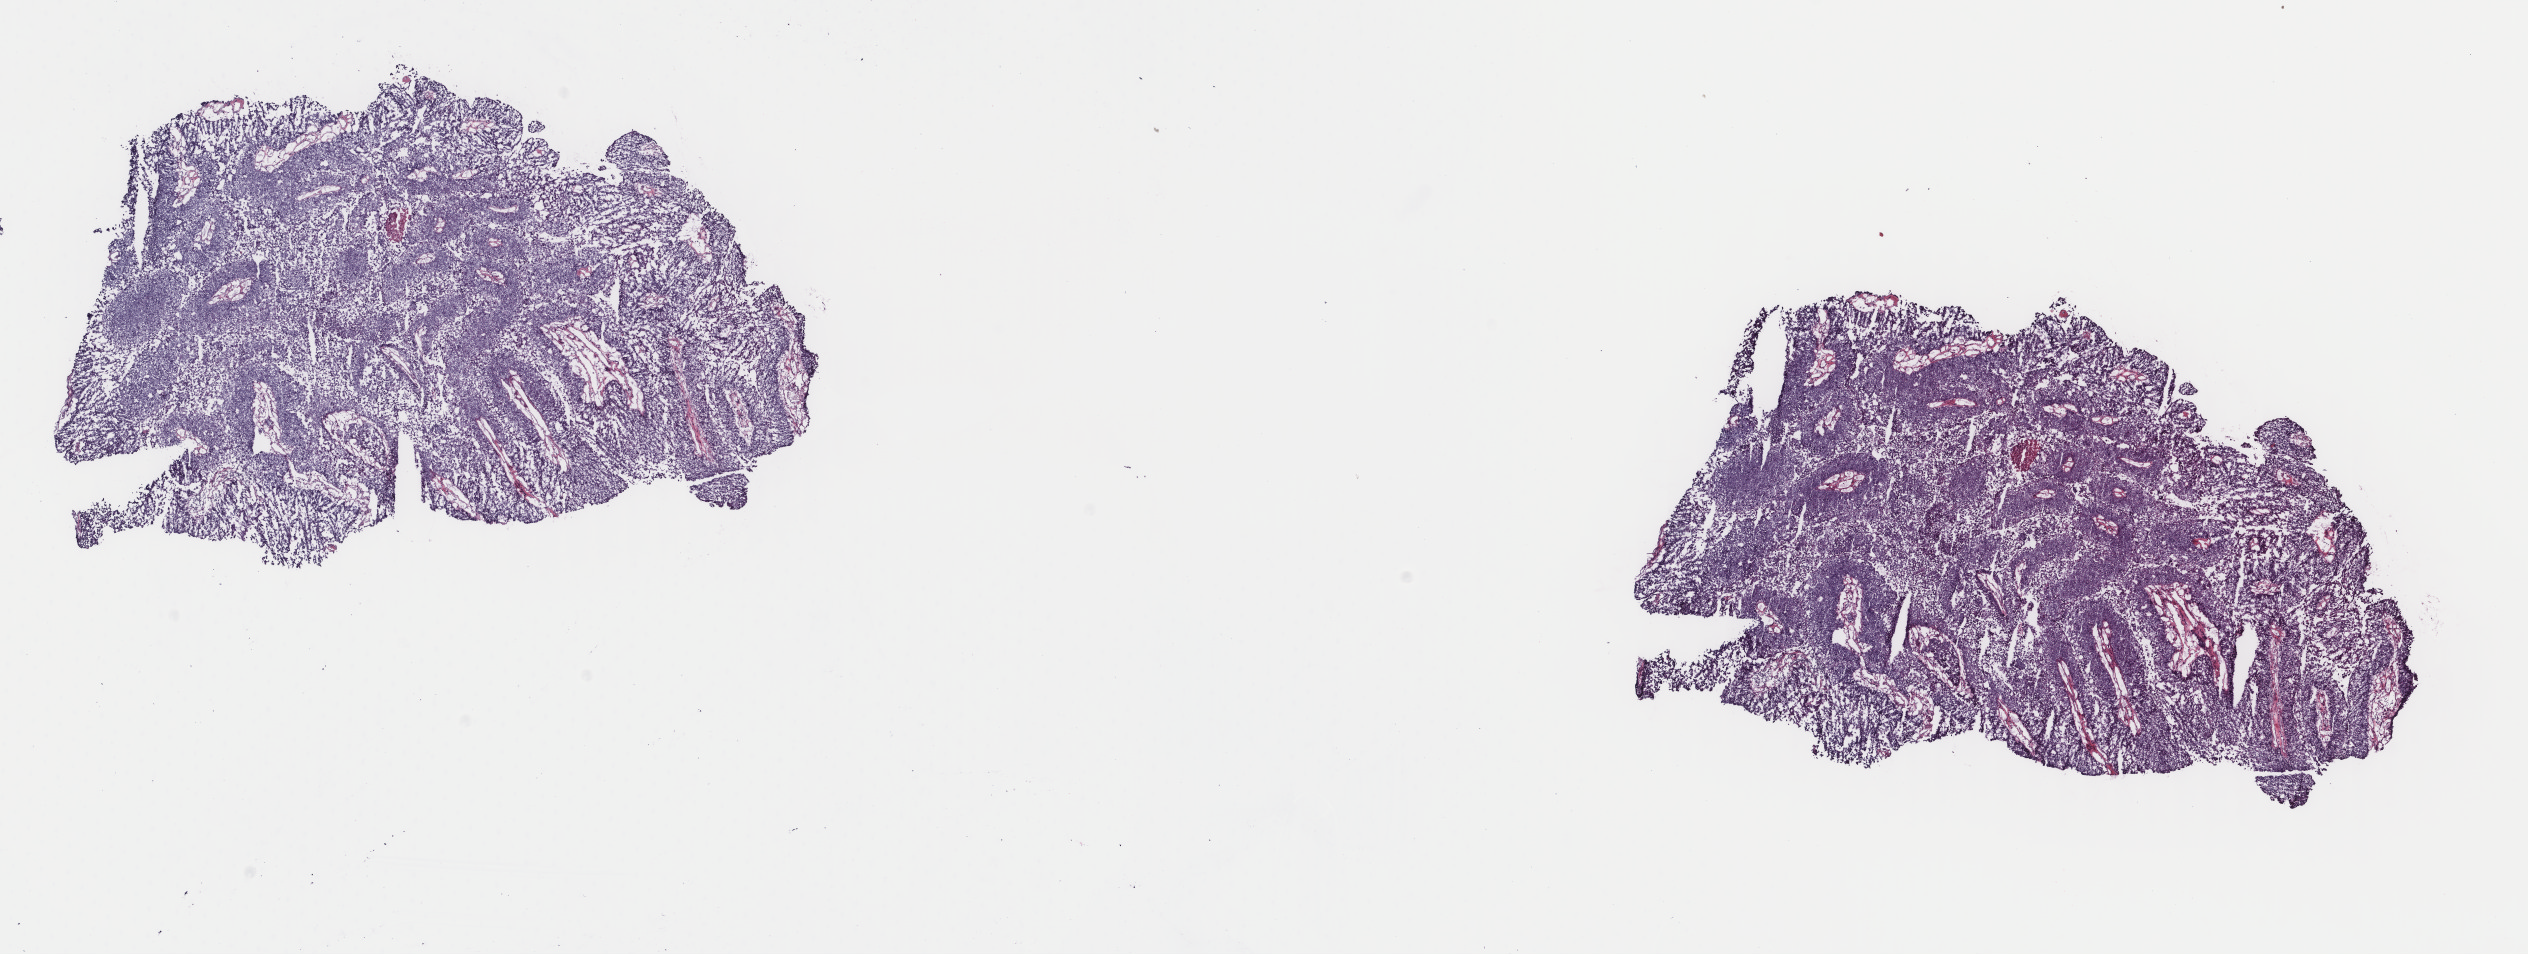
Digitized H&E tissue section (whole slide), a low-resolution overview of the entire scanned area, about 20.1 x 7.6 mm (slide scanned at 40x). Frozen section from the top of the tissue portion. Bladder, primary tumour sample. Patient: male, age at initial diagnosis 60 years. Histologic grade: low grade. Pathologist review of this section (percent, as recorded): tumour cells 95%, tumour nuclei 80%, normal cells 0%, stromal cells 0%, necrosis 5%. Infiltration values recorded for this section: lymphocyte infiltration 3%, monocyte infiltration 1%, neutrophil infiltration 0%.
• diagnosis: Papillary transitional cell carcinoma
• AJCC pathologic stage: II (7th edition)